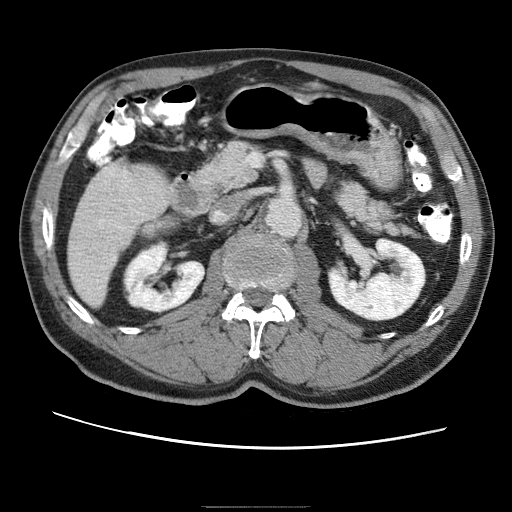
Contrast-enhanced abdominal CT (liver protocol), one axial slice; slice 14 of 75 in the series (ordered by position); reconstruction kernel STANDARD; 120 kVp; one of 2 acquisitions stored at this slice position; soft-tissue window (W 400 / L 40 HU); 512 × 512 image matrix. Case-level facts recorded for this patient, not image findings: diagnosis: hepatocellular carcinoma (patient treated with transarterial chemoembolisation; whether this scan precedes or follows treatment is not stated here); TNM stage (as recorded): Stage-II; Child-Pugh class: A; tumour nodularity: multinodular; tumour size: 2 cm.
Outlined on this slice (semi-automatic segmentation, software-assisted and operator-edited):
- liver parenchyma outside the tumour (the mass and vessels are separate outlines, so this box may not span the whole liver): bounding box [x1, y1, x2, y2] px = [68, 166, 138, 302]
- liver vessels: [82, 170, 114, 210]